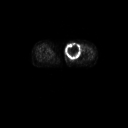
FDG PET of an extremity soft-tissue mass (from a PET/CT study), one axial slice; slice 33 of 91 in the series (ordered by position); 3.27 mm slice thickness; 128 × 128 image matrix. Female patient, age 74 years. From the clinical record (not read from this slice): histological type: pleomorphic leiomyosarcoma; grade: high; site of the primary tumour: left thigh.
Annotated regions visible in this slice (expert contour drawn on MRI and transferred to this co-registered scan by the dataset authors):
- gross tumour volume including surrounding oedema: box from (x=65, y=42) to (x=82, y=60) px
- gross tumour volume (mass): (x=65, y=42)–(x=82, y=60)